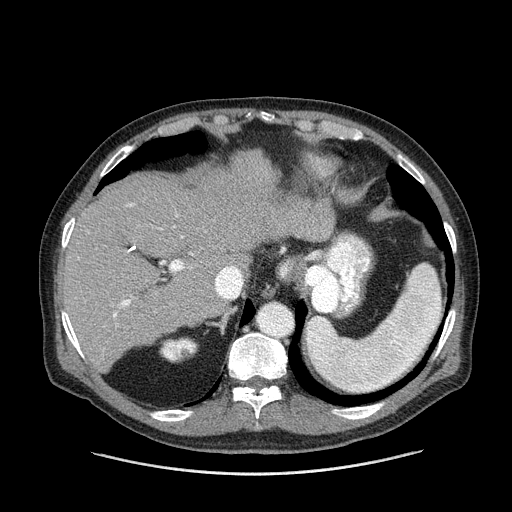
Contrast-enhanced abdominal CT (liver protocol), one axial slice; position 106 of 180 along the scan axis; reconstruction kernel STANDARD; one of 2 acquisitions stored at this slice position; soft-tissue window (W 400 / L 40 HU); 2.5 mm slice thickness; 512 × 512 image matrix. From the clinical record (not read from this slice): diagnosis: hepatocellular carcinoma (patient treated with transarterial chemoembolisation; whether this scan precedes or follows treatment is not stated here); TNM stage (as recorded): Stage-II; Child-Pugh class: A; tumour size: 2.8 cm.
Structures marked on this image (semi-automatically segmented with operator editing):
- liver parenchyma outside the tumour (the mass and vessels are separate outlines, so this box may not span the whole liver): box from (x=62, y=152) to (x=334, y=370) px
- liver vessels: (x=113, y=204)–(x=193, y=317)